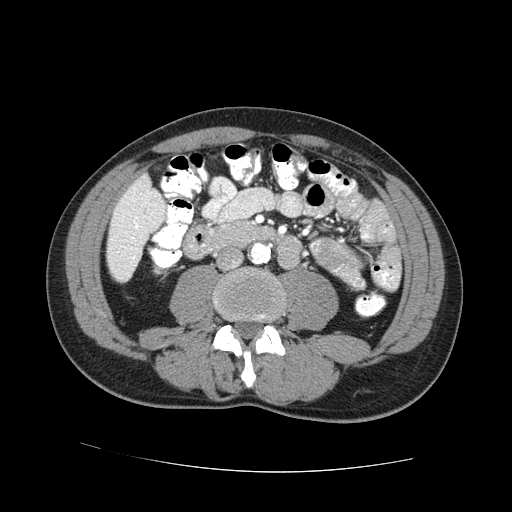
Contrast-enhanced abdominal CT (liver protocol), one axial slice. 100 kVp. One of 2 acquisitions stored at this slice position. Soft-tissue window (W 400 / L 40 HU). 512 × 512 image matrix, field of view 380 × 380 mm. From the clinical record (not read from this slice): diagnosis: hepatocellular carcinoma (patient treated with transarterial chemoembolisation; whether this scan precedes or follows treatment is not stated here); TNM stage (as recorded): Stage-IVA; Child-Pugh class: A; tumour differentiation: no biopsy.
Outlined on this slice (semi-automatically segmented with operator editing):
- liver parenchyma outside the tumour (the mass and vessels are separate outlines, so this box may not span the whole liver): bounding box (x1, y1, x2, y2) in pixels: (106, 174, 166, 282)
- liver vessels: (133, 217, 138, 259)